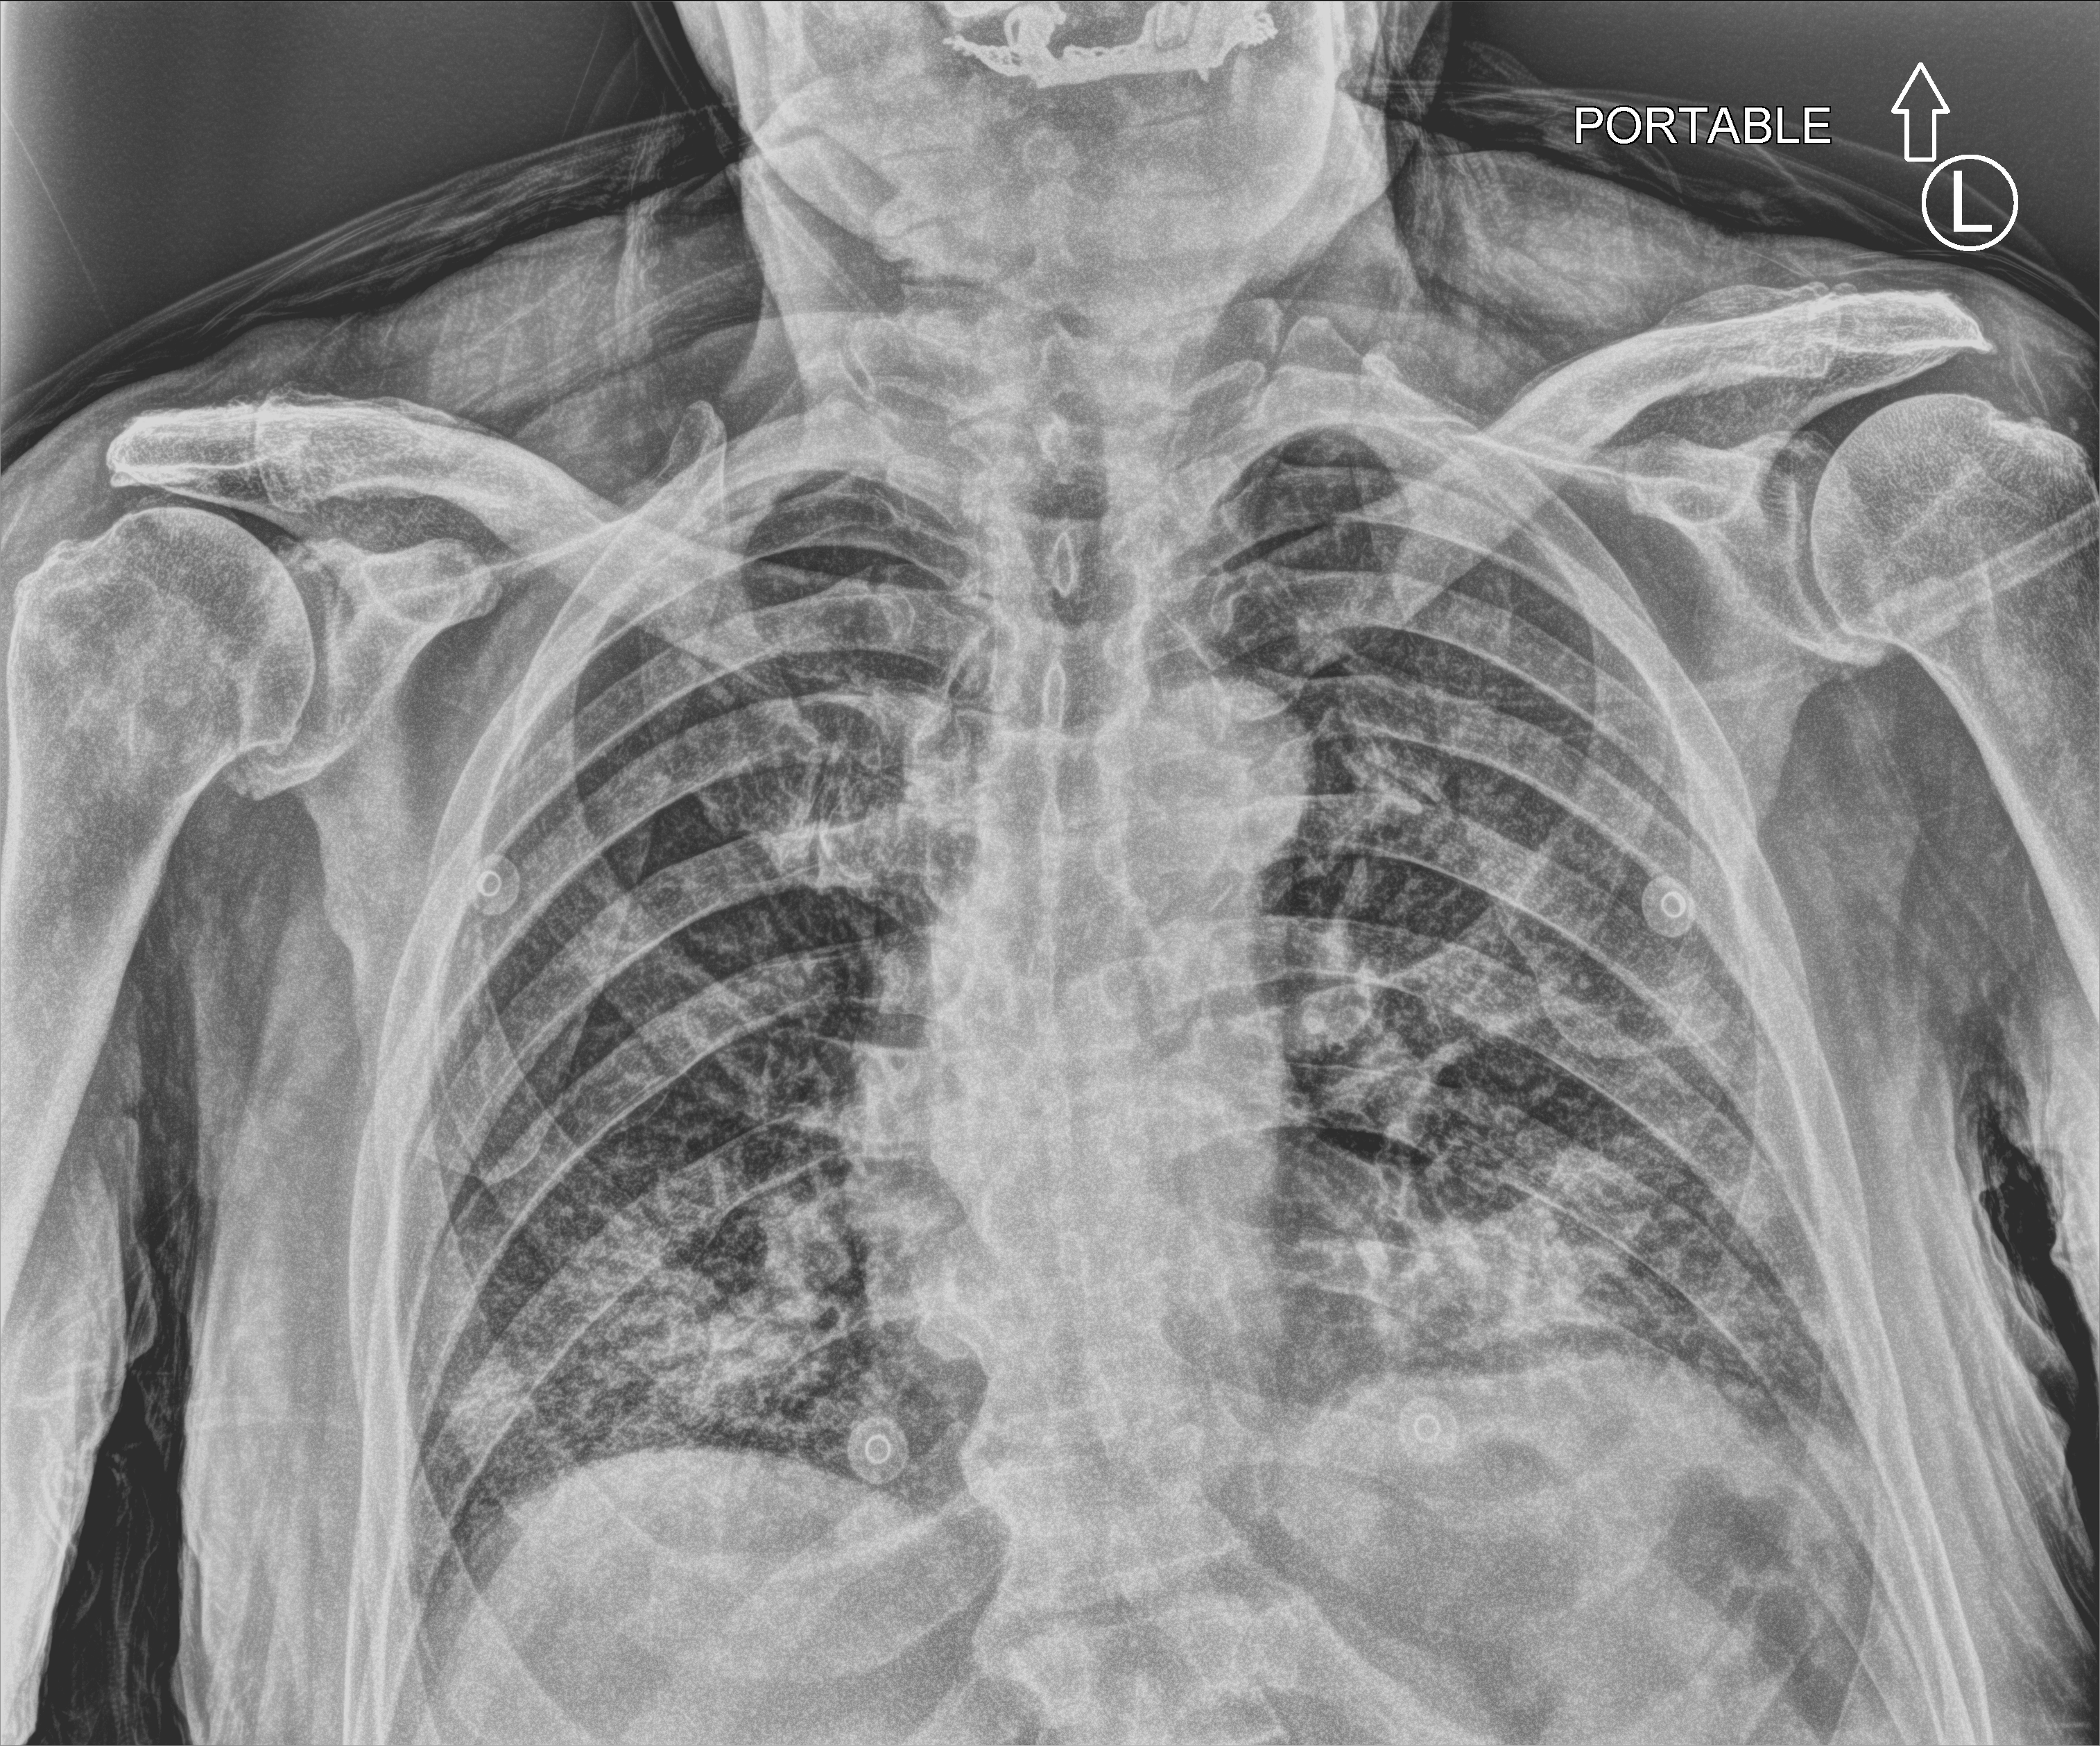
Portable chest radiograph. Male patient hospitalised with COVID-19, age 75–90 years.
Admission-level facts for this patient (not findings on this image; timing relative to this image not recorded): chronic kidney disease (admission record): no.